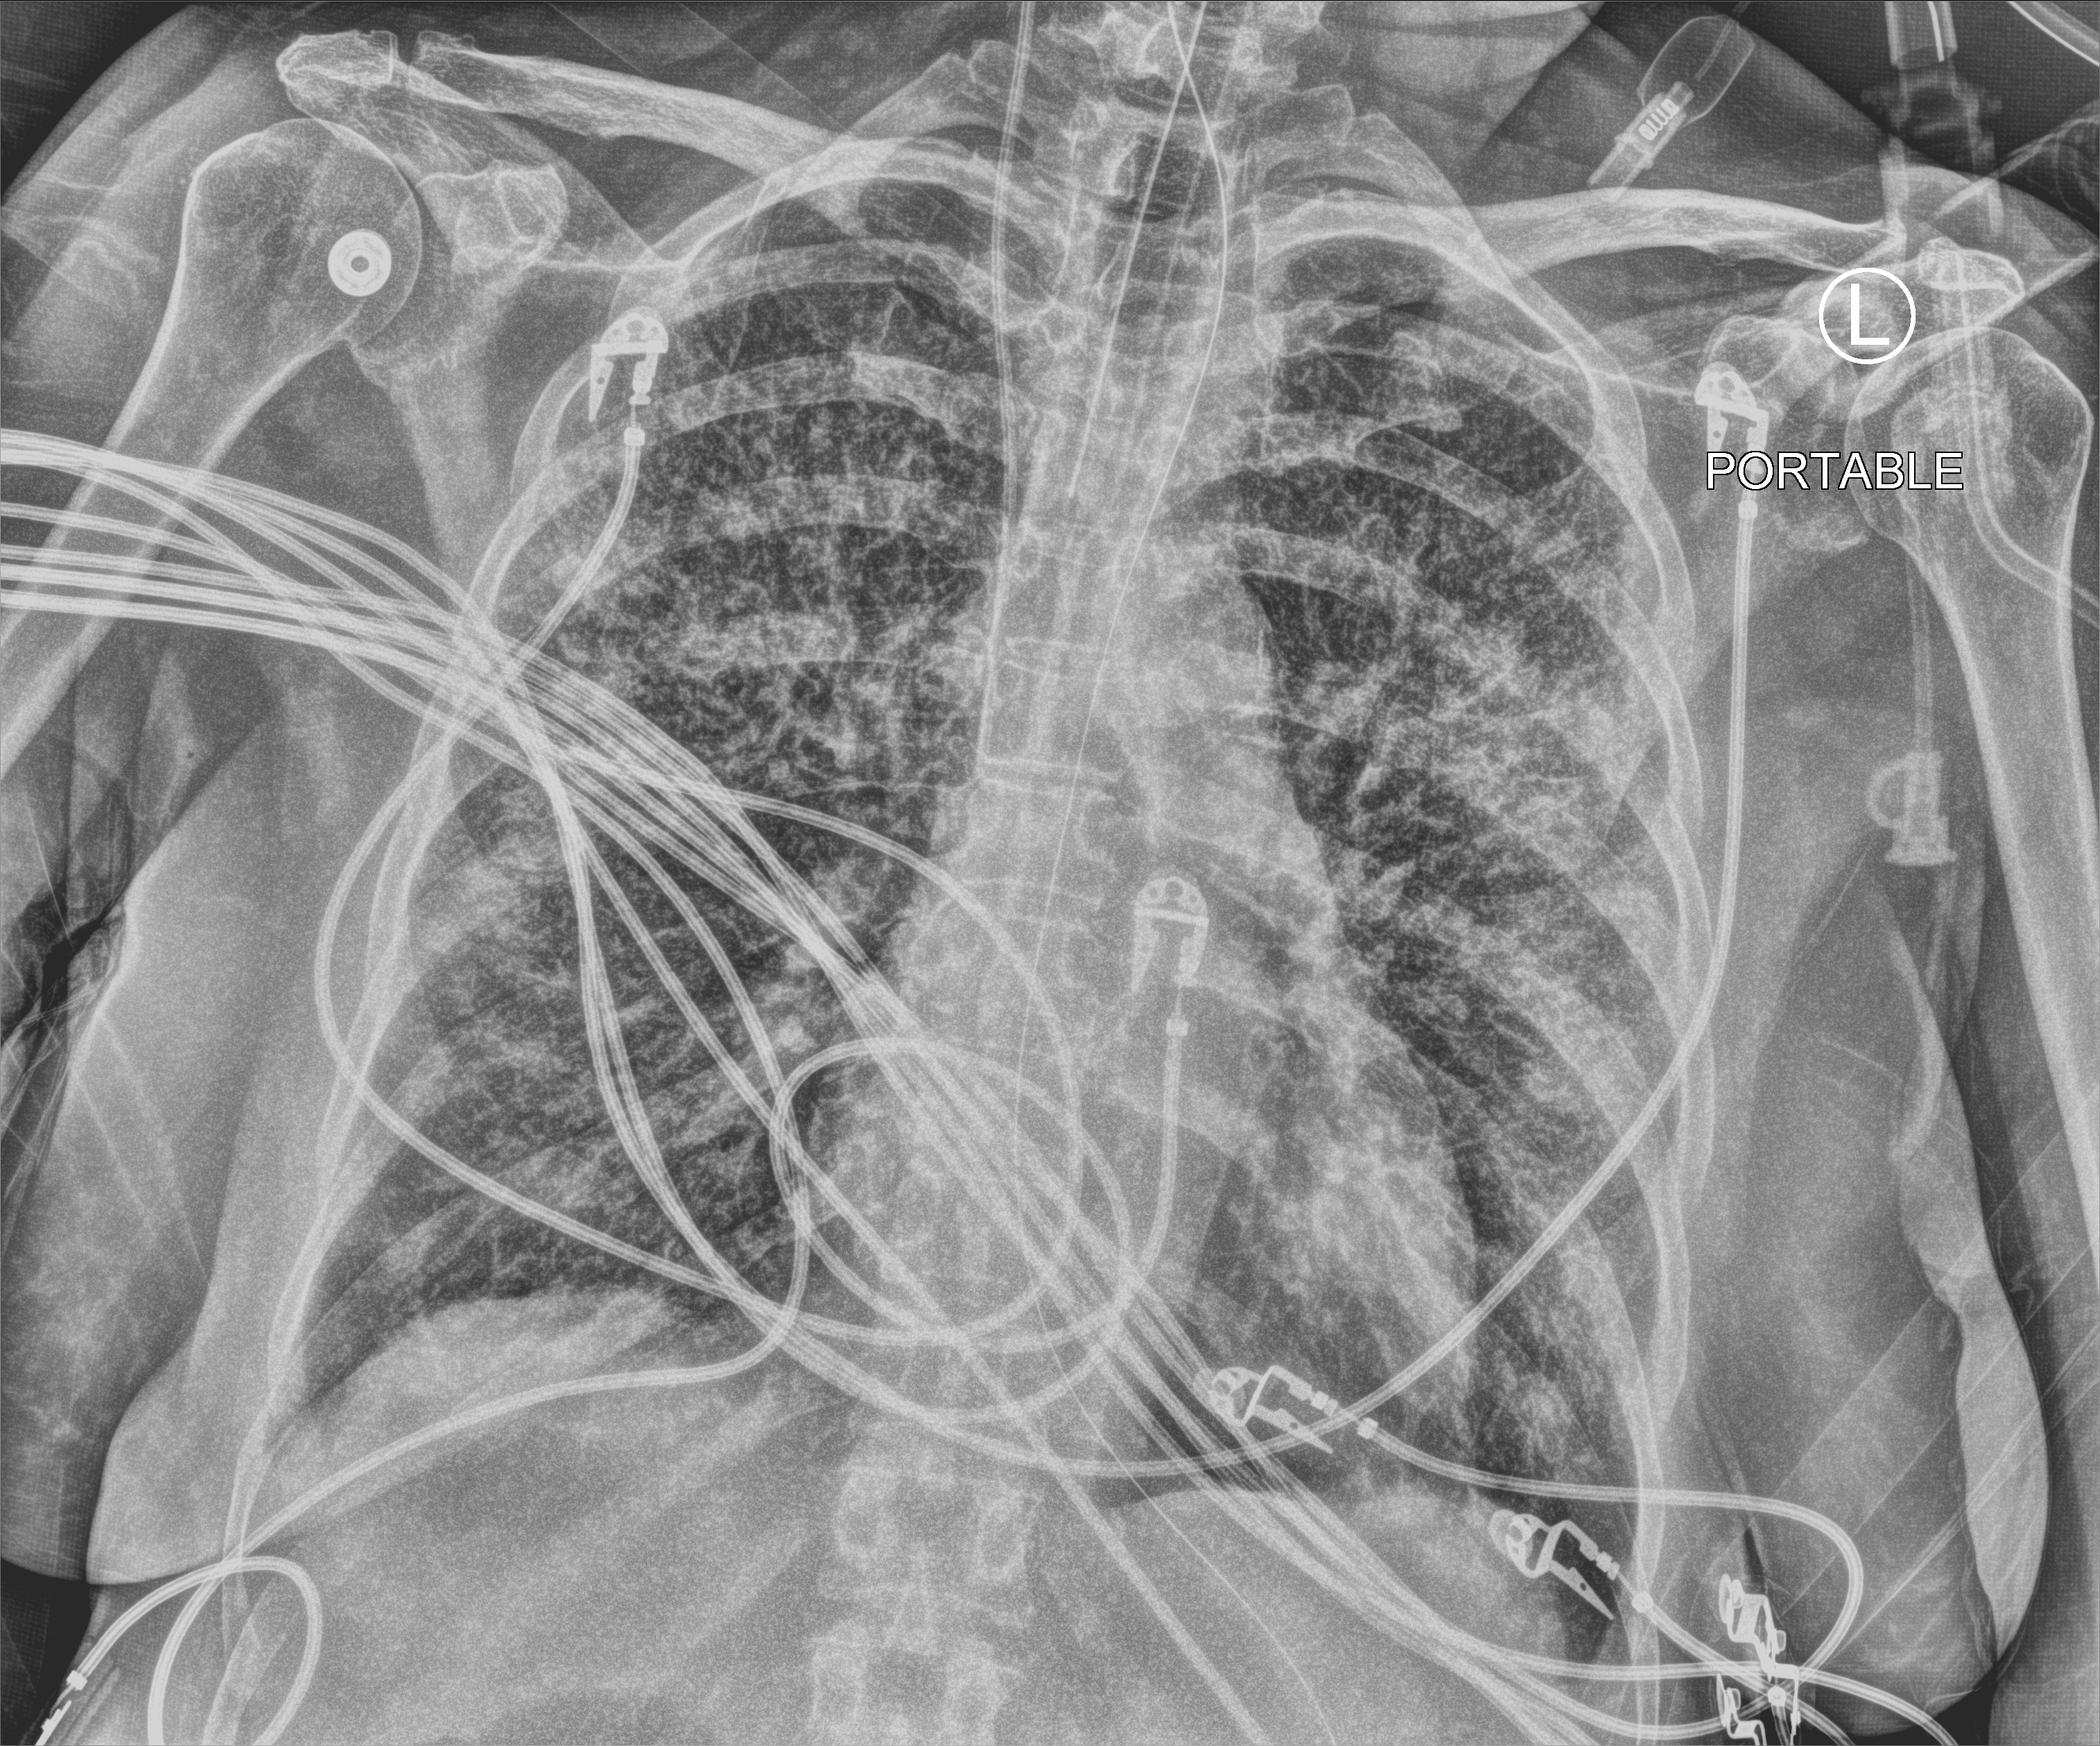
Bedside chest radiograph (computed radiography). Patient hospitalised with COVID-19; female, aged 60–74 years.
Hospital-stay facts (about this admission, not read from this image; timing relative to this image not recorded): COPD (admission record): no.